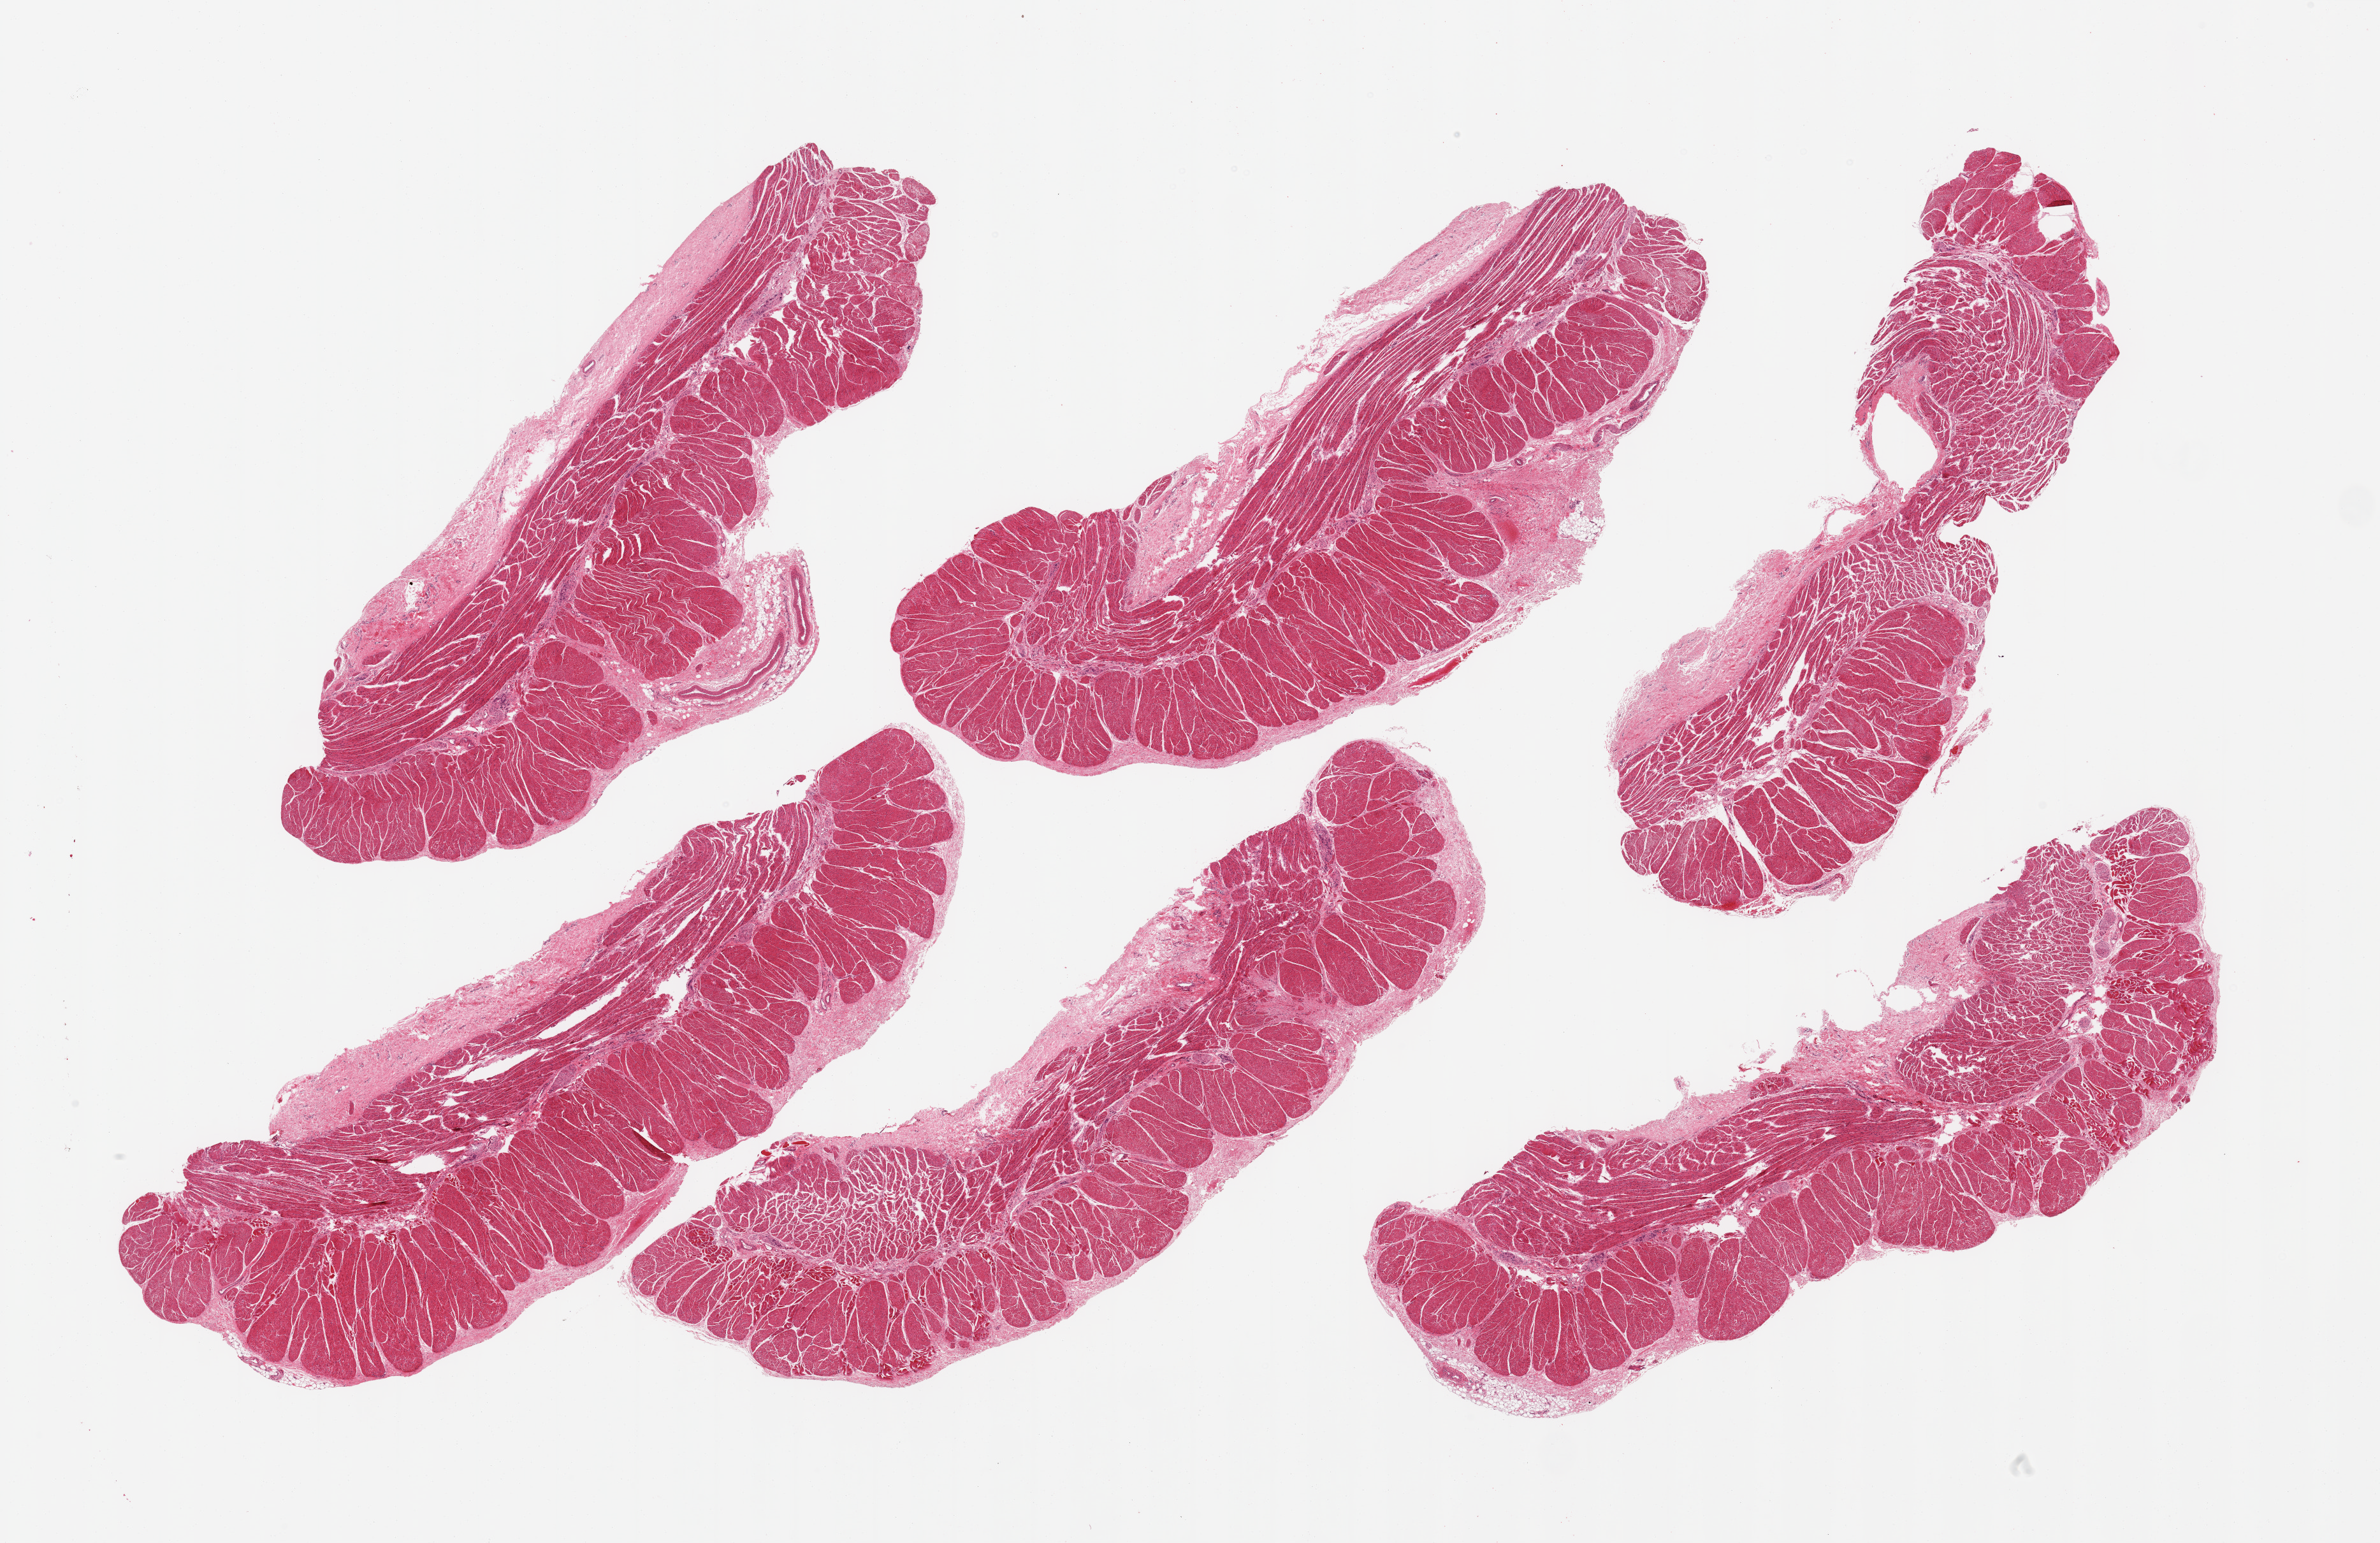
H&E whole-slide image, a low-resolution overview of the entire scanned area, about 29.5 x 19.1 mm; PAXgene-fixed paraffin-embedded (PFPE) section; sampled site (target tissue): esophageal muscle; donor tissue sample. Donor sex: female.
Pathologist's review note for this sample: 6 pieces, confirmed target muscularis.